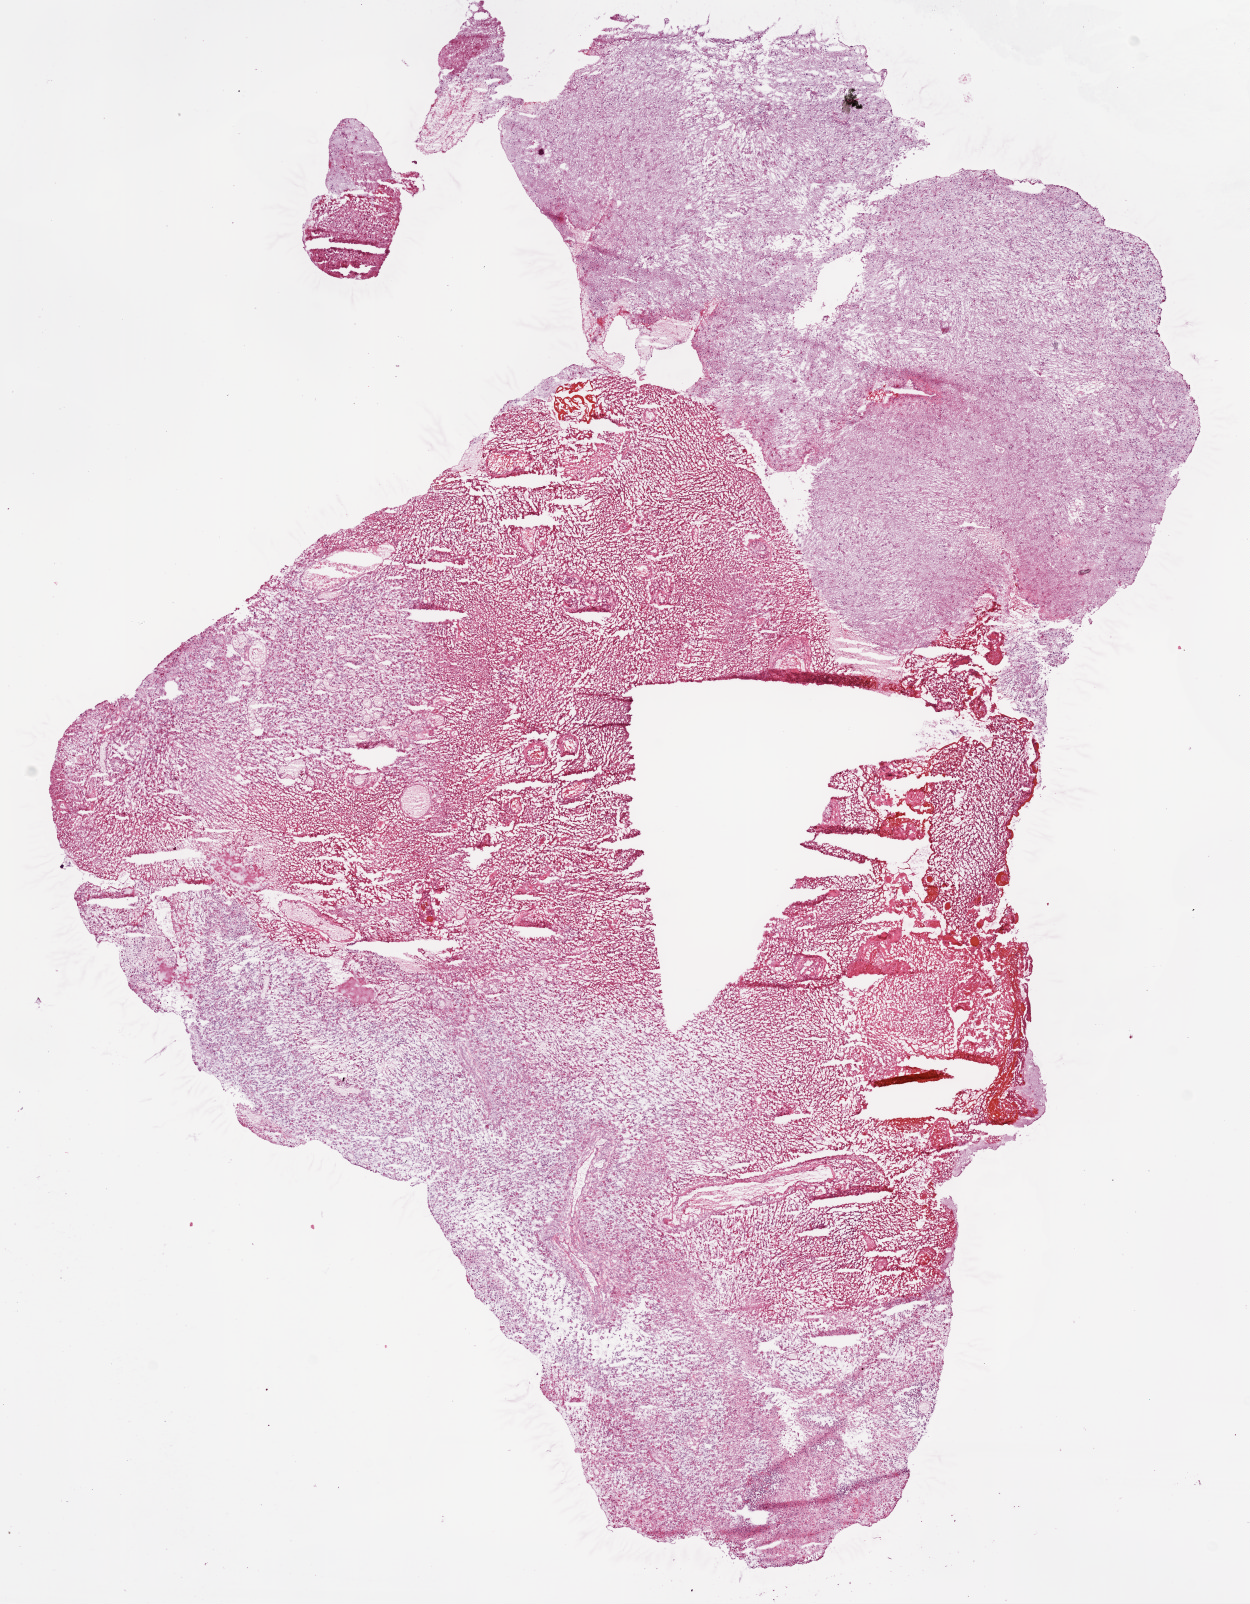
Digitized H&E-stained tissue section (whole slide), shown as a low-resolution overview of the whole scanned area (about 10.0 x 12.9 mm). Frozen section from the bottom of the tissue portion. Sample: primary tumour, brain. Male patient; age at initial diagnosis 58 years.
Histologic diagnosis: Glioblastoma.